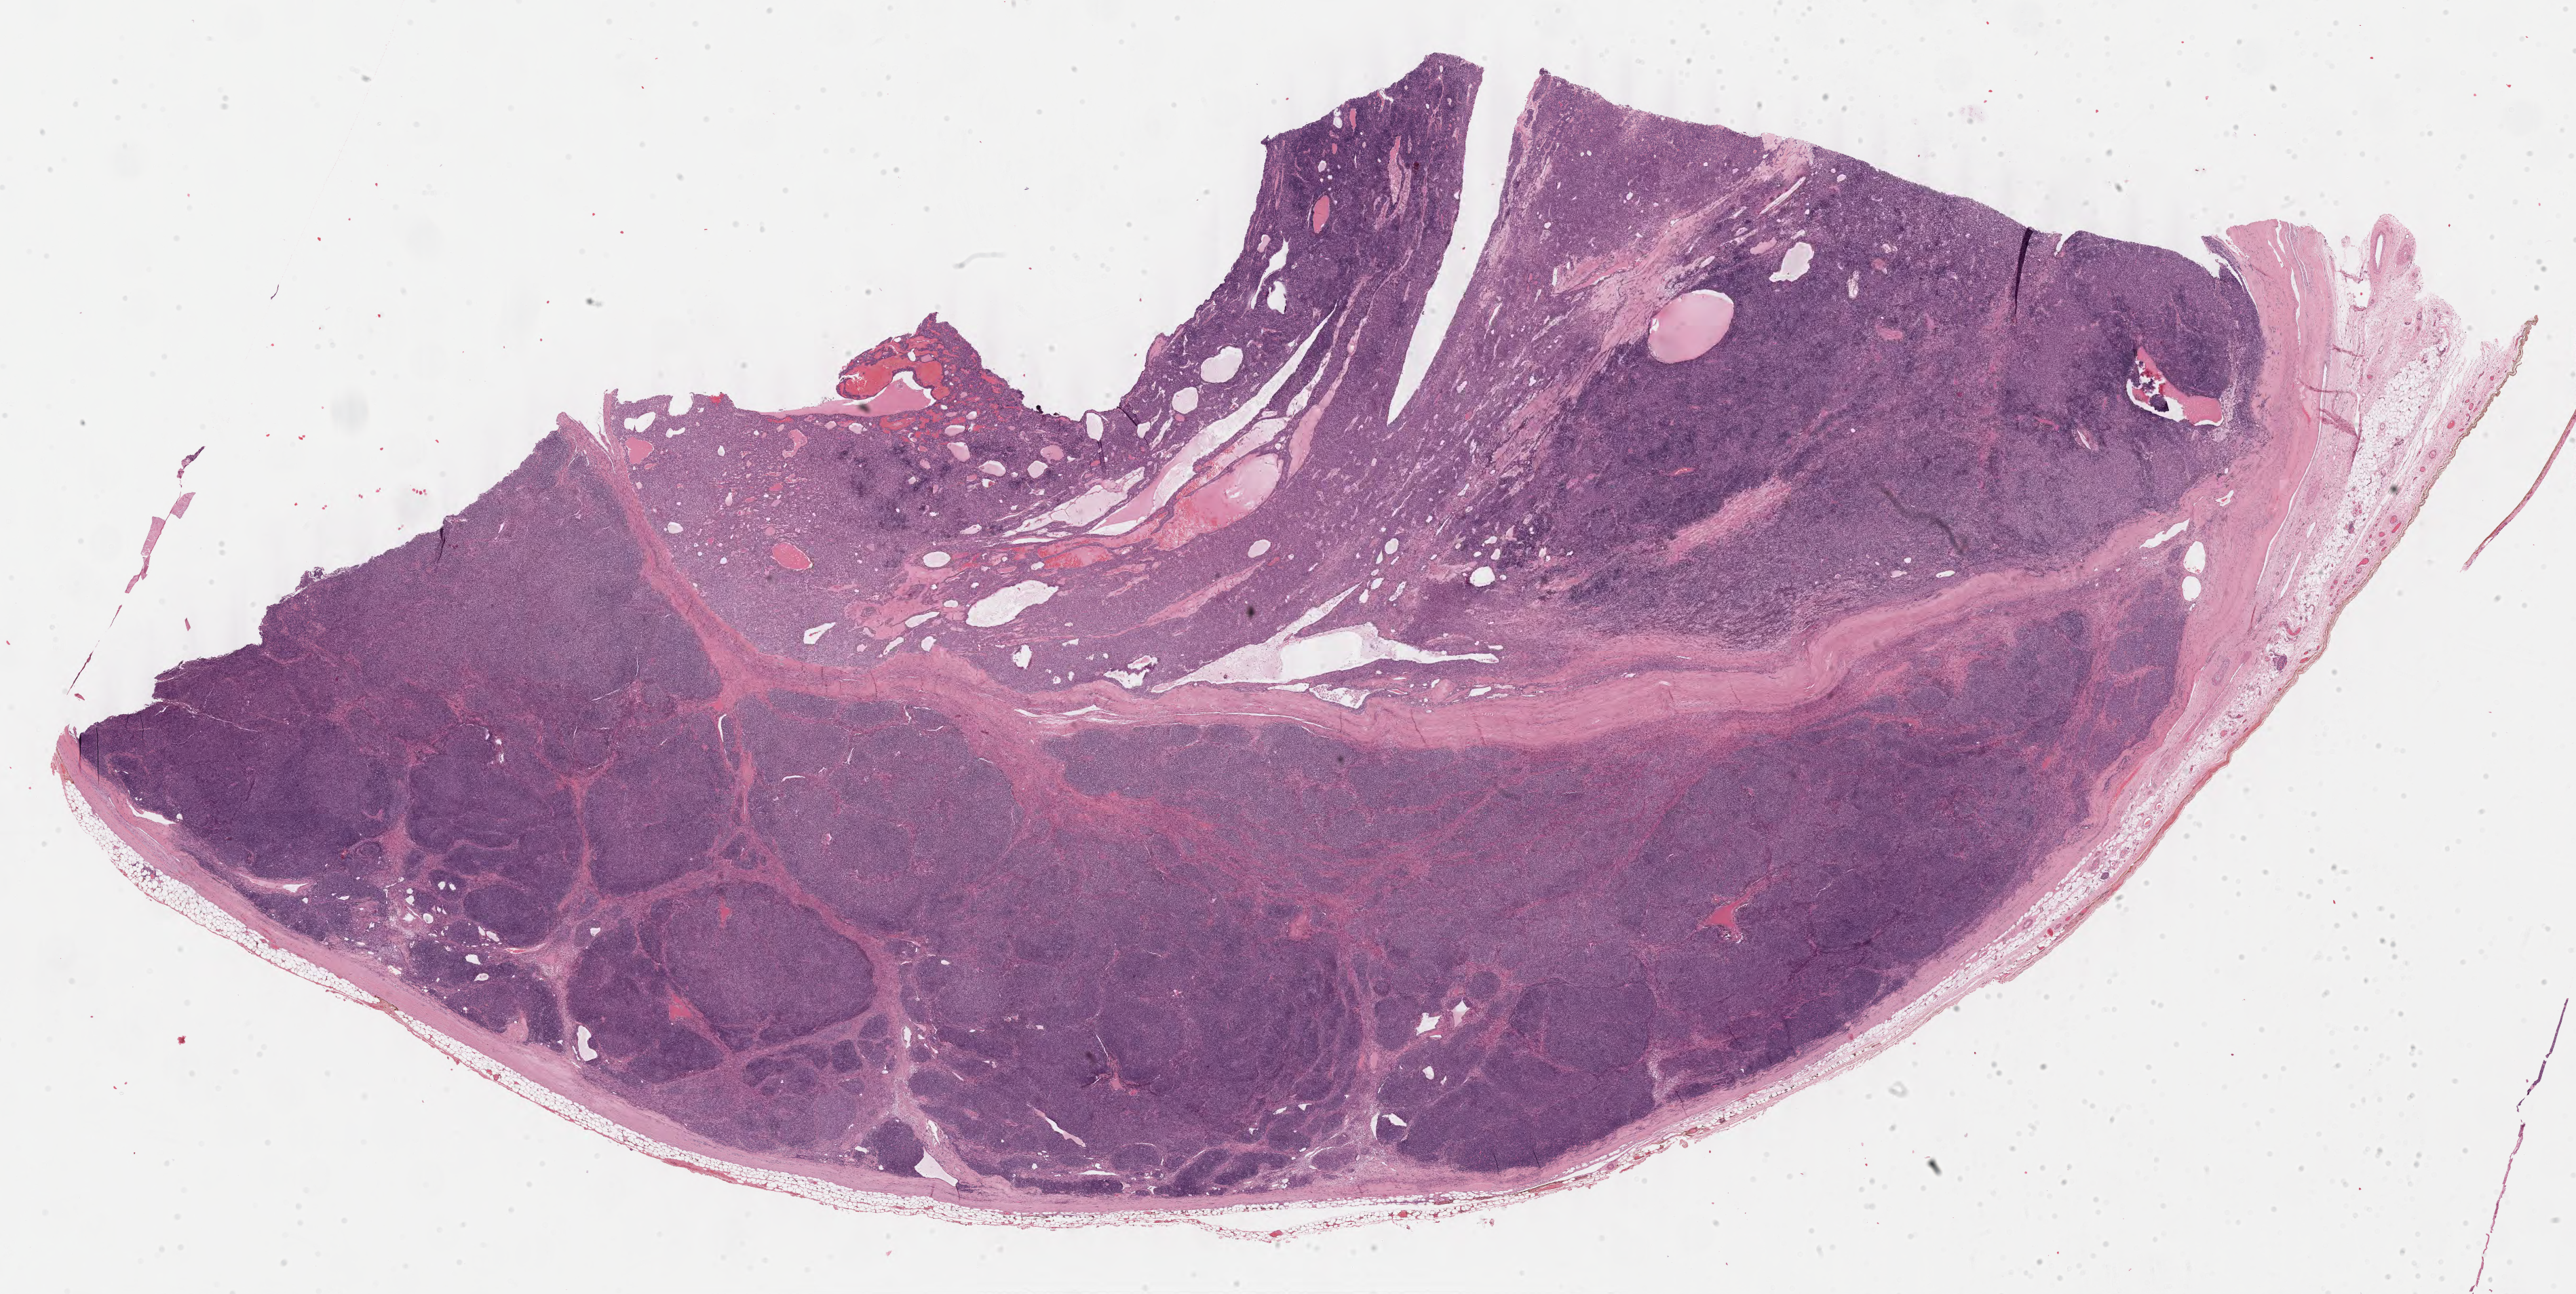
H&E whole-slide image — whole scanned area (about 30.0 x 15.1 mm, from a 40x scan) shown as a low-resolution overview, formalin-fixed paraffin-embedded (FFPE) diagnostic section, sample: primary tumour, thymus. Female patient; age at initial diagnosis 81 years.
• histologic diagnosis: Thymoma, type AB, malignant